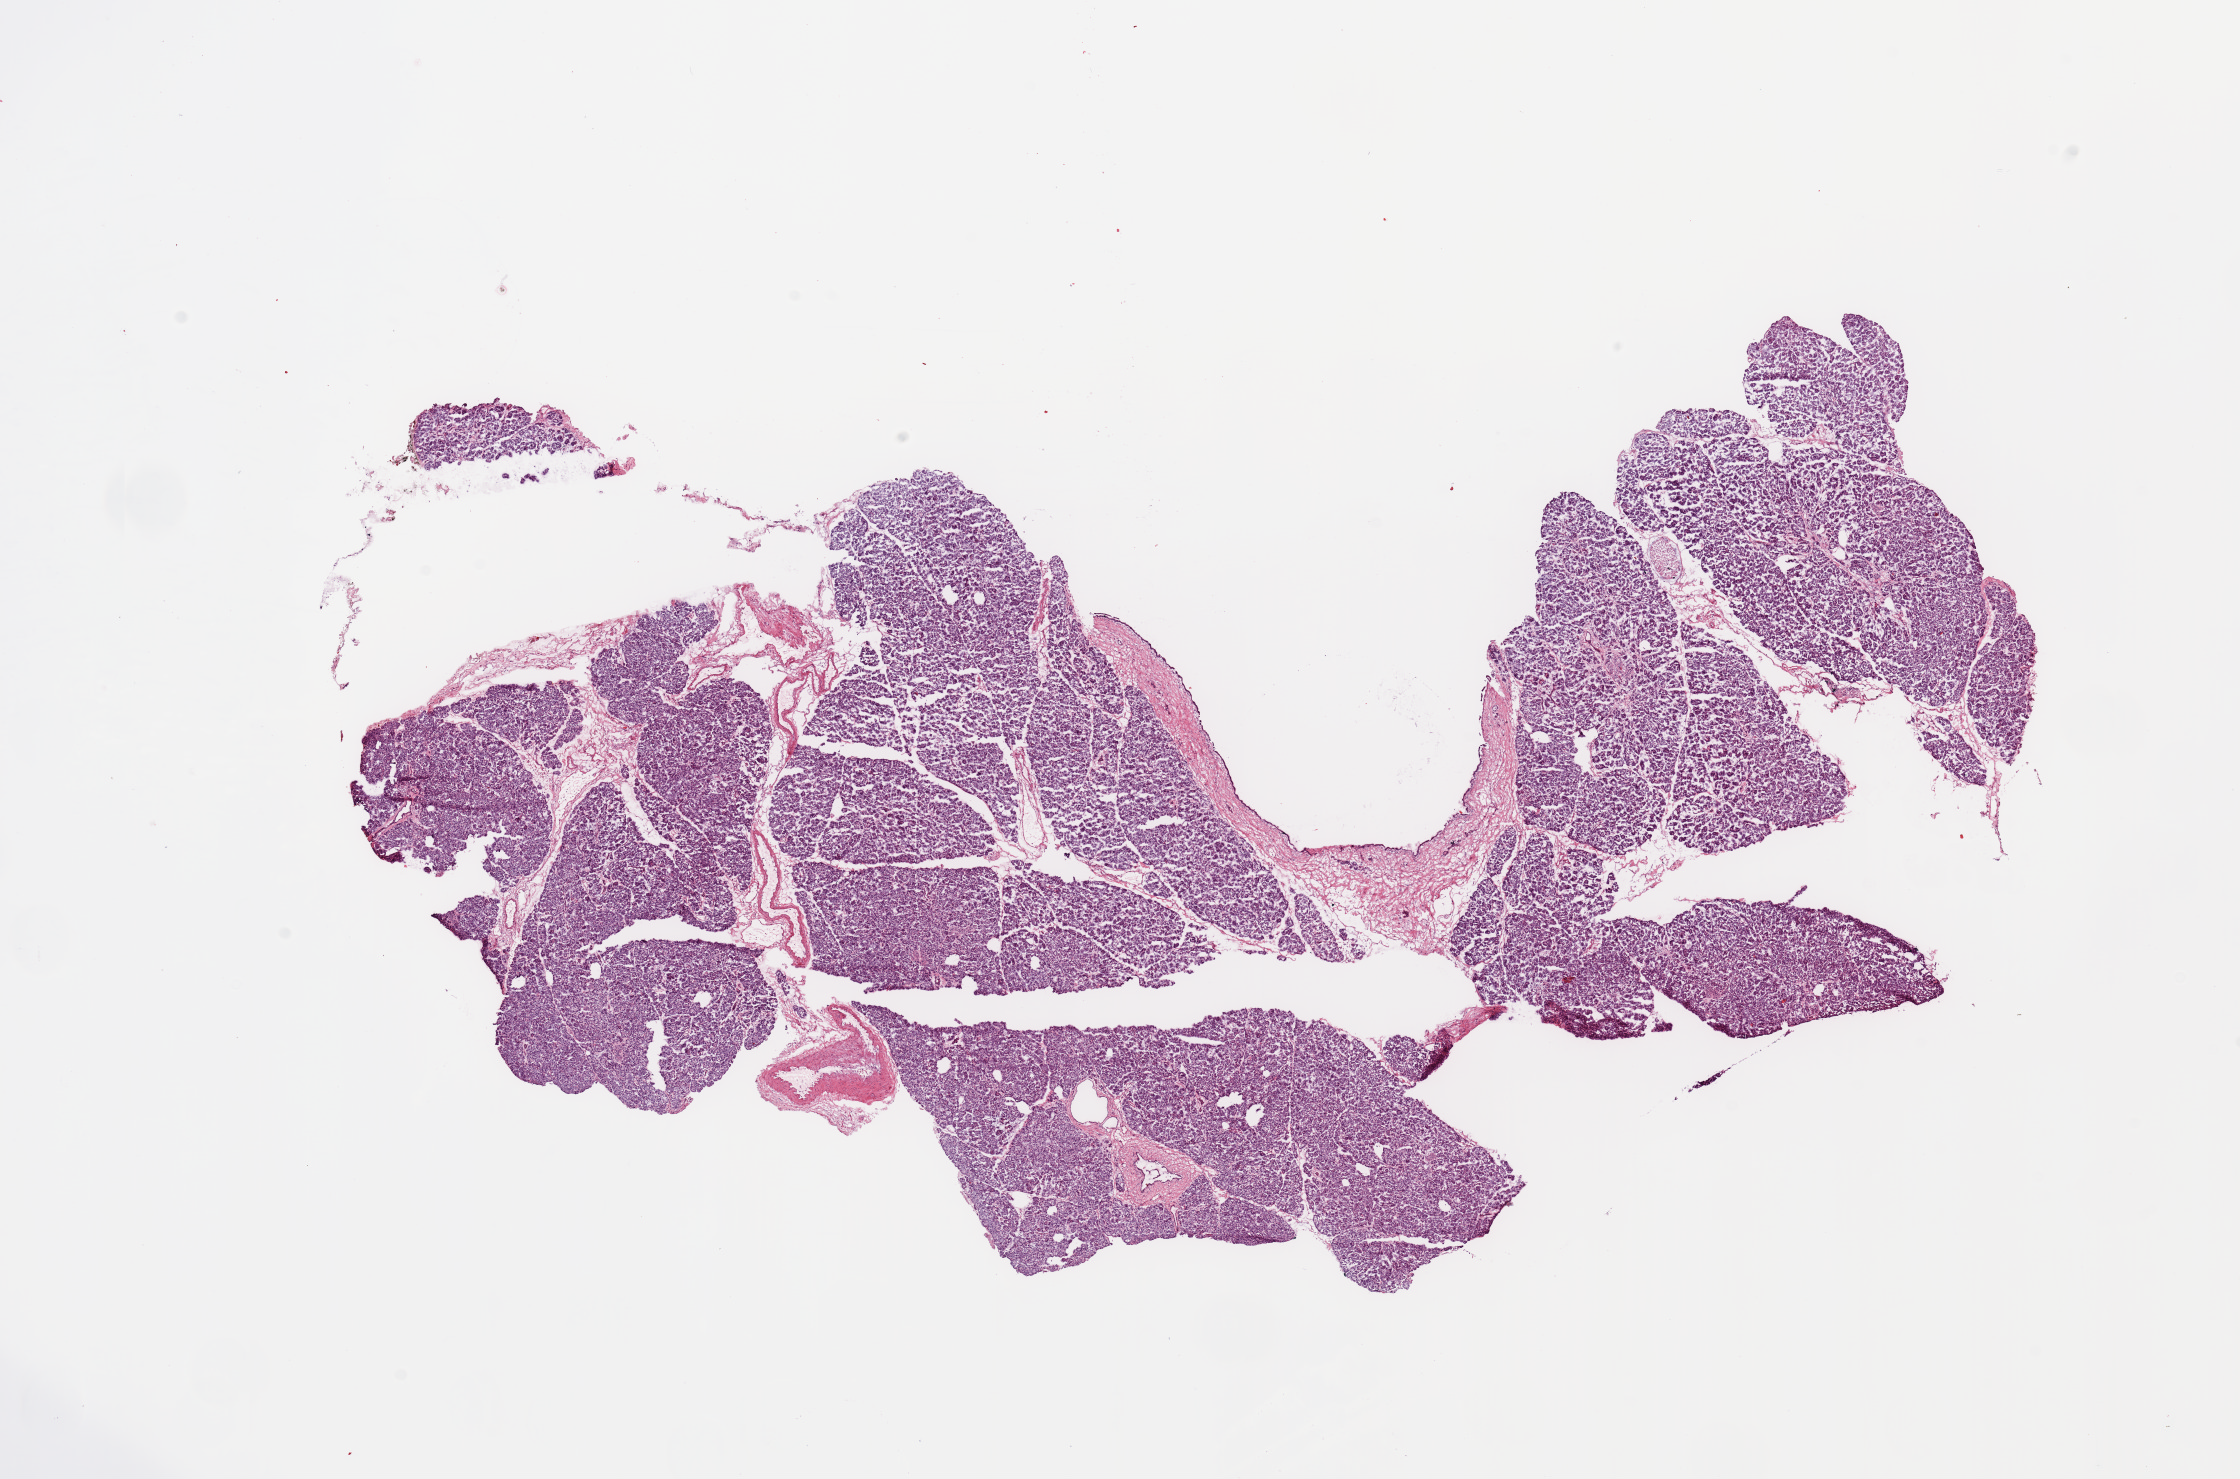
H&E whole-slide image — a low-resolution overview of the entire scanned area, about 17.7 x 11.7 mm, normal (non-tumour) tissue sample, pancreas. Male, 69 y/o.
This section: normal (non-tumour) tissue from the same patient. Patient diagnosis: Infiltrating duct carcinoma, NOS.